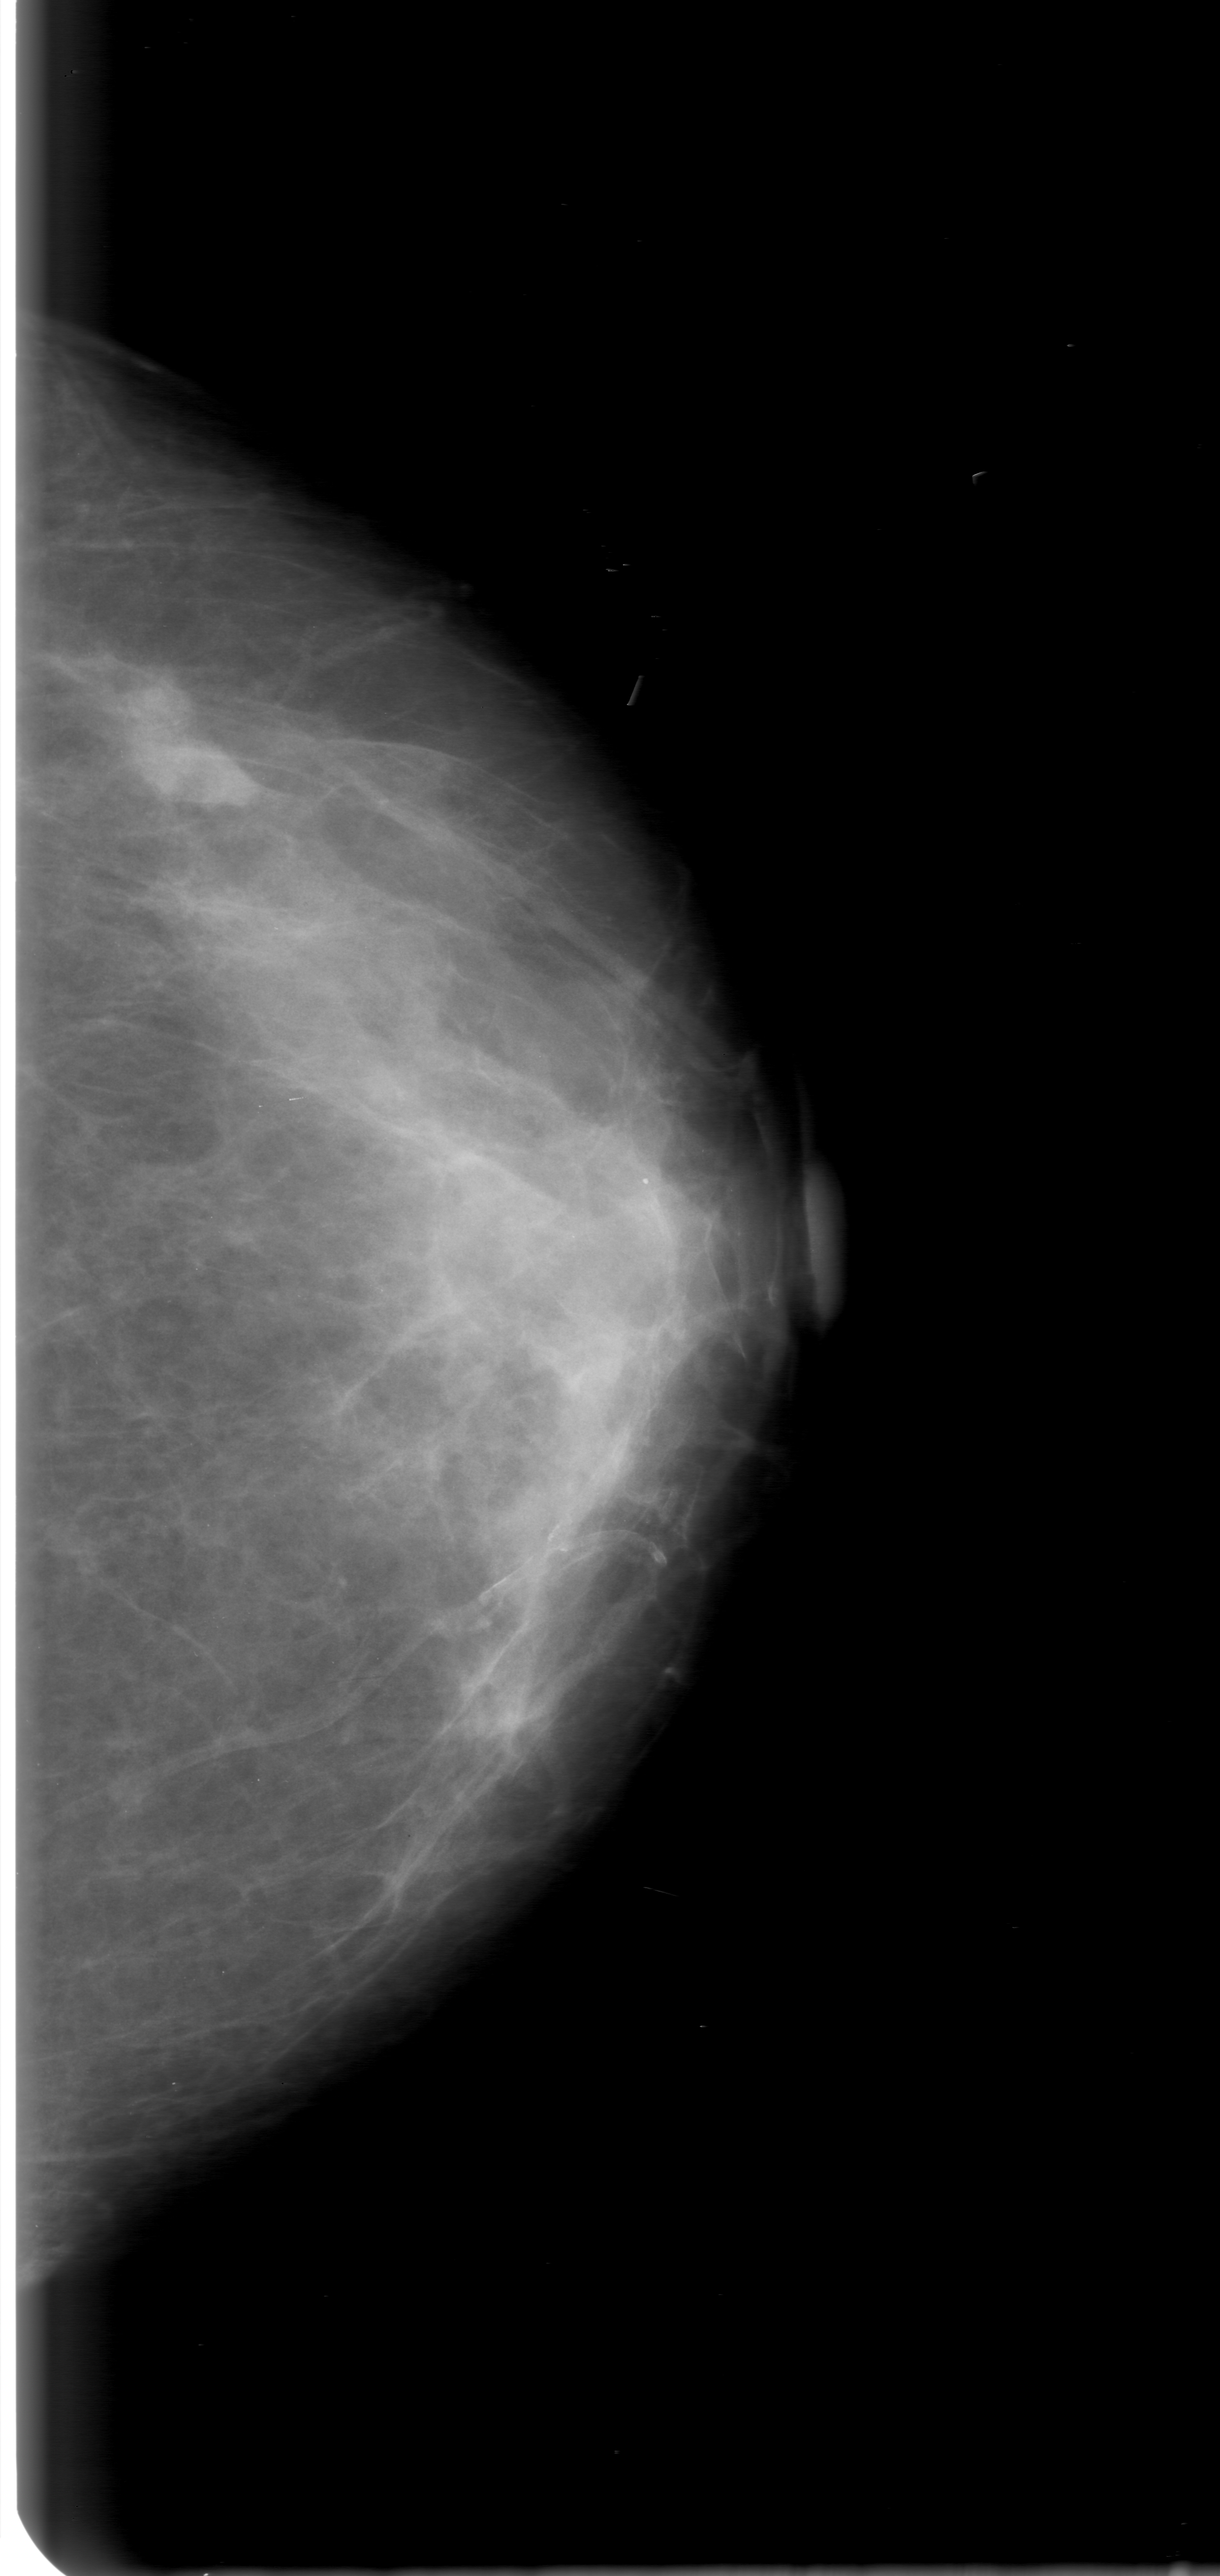
Digitized screen-film mammogram; left breast; craniocaudal (CC) view; 1220 × 2576 image matrix.
Expert-marked regions of interest on this film, with their recorded descriptors:
- mass, shape lobulated, margins obscured; BI-RADS assessment category 0; pathology result (as recorded, not read from the image): malignant: bounding box (x1, y1, x2, y2) in pixels: (95, 642, 252, 814)